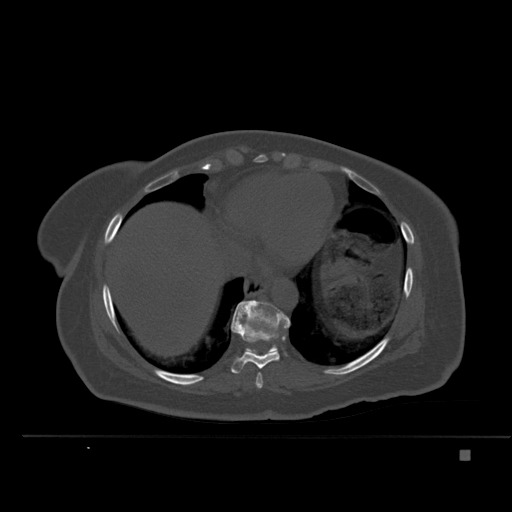
CT including the spine, one axial slice. Slice 295 of 477 in the series (ordered by position). Bone window (W 1800 / L 400 HU). 512 × 512 image matrix, field of view 422 × 422 mm. Female patient, age 74 years. Case-level facts recorded for this patient, not image findings: primary cancer: colon.
Structures marked on this image (semi-automatic segmentation, software-assisted and operator-edited):
- T10 vertebra: bounding box <239,300,287,352> (left, top, right, bottom; pixels)
- T8 vertebra: <256,373,263,389>
- T9 vertebra: <231,305,290,374>